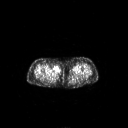
FDG PET of an extremity soft-tissue mass (from a PET/CT study), one axial slice. Position 238 of 311 along the scan axis. 3.27 mm slice thickness. 128 × 128 image matrix. Patient: female, 78 years. Case-level facts recorded for this patient, not image findings: histological type: leiomyosarcoma; grade: intermediate; site of the primary tumour: parascapusular.
Outlined on this slice (expert contour drawn on MRI and transferred to this co-registered scan by the dataset authors):
- gross tumour volume including surrounding oedema: box from (x=52, y=65) to (x=61, y=75) px
- gross tumour volume (mass): (x=52, y=65)–(x=61, y=75)